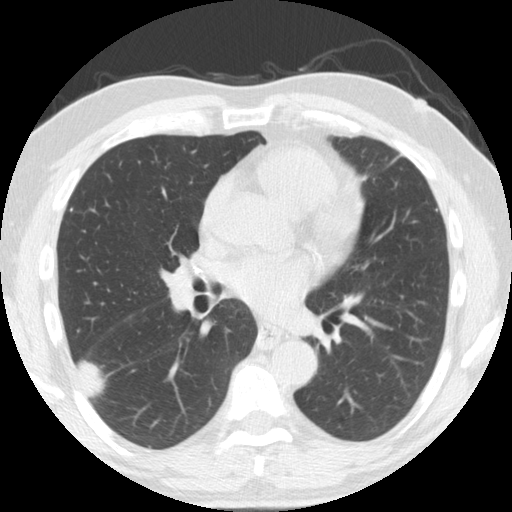
Low-dose screening chest CT, one axial slice; slice 86 of 174 in the series (ordered by position); reconstruction kernel STANDARD; lung window (W 1500 / L -600 HU); 512 × 512 image matrix, field of view 341 × 341 mm.
Outlined on this slice (expert manual segmentation):
- lesion 1 (tumor, lower lobe of right lung): box from (x=77, y=361) to (x=105, y=398) px